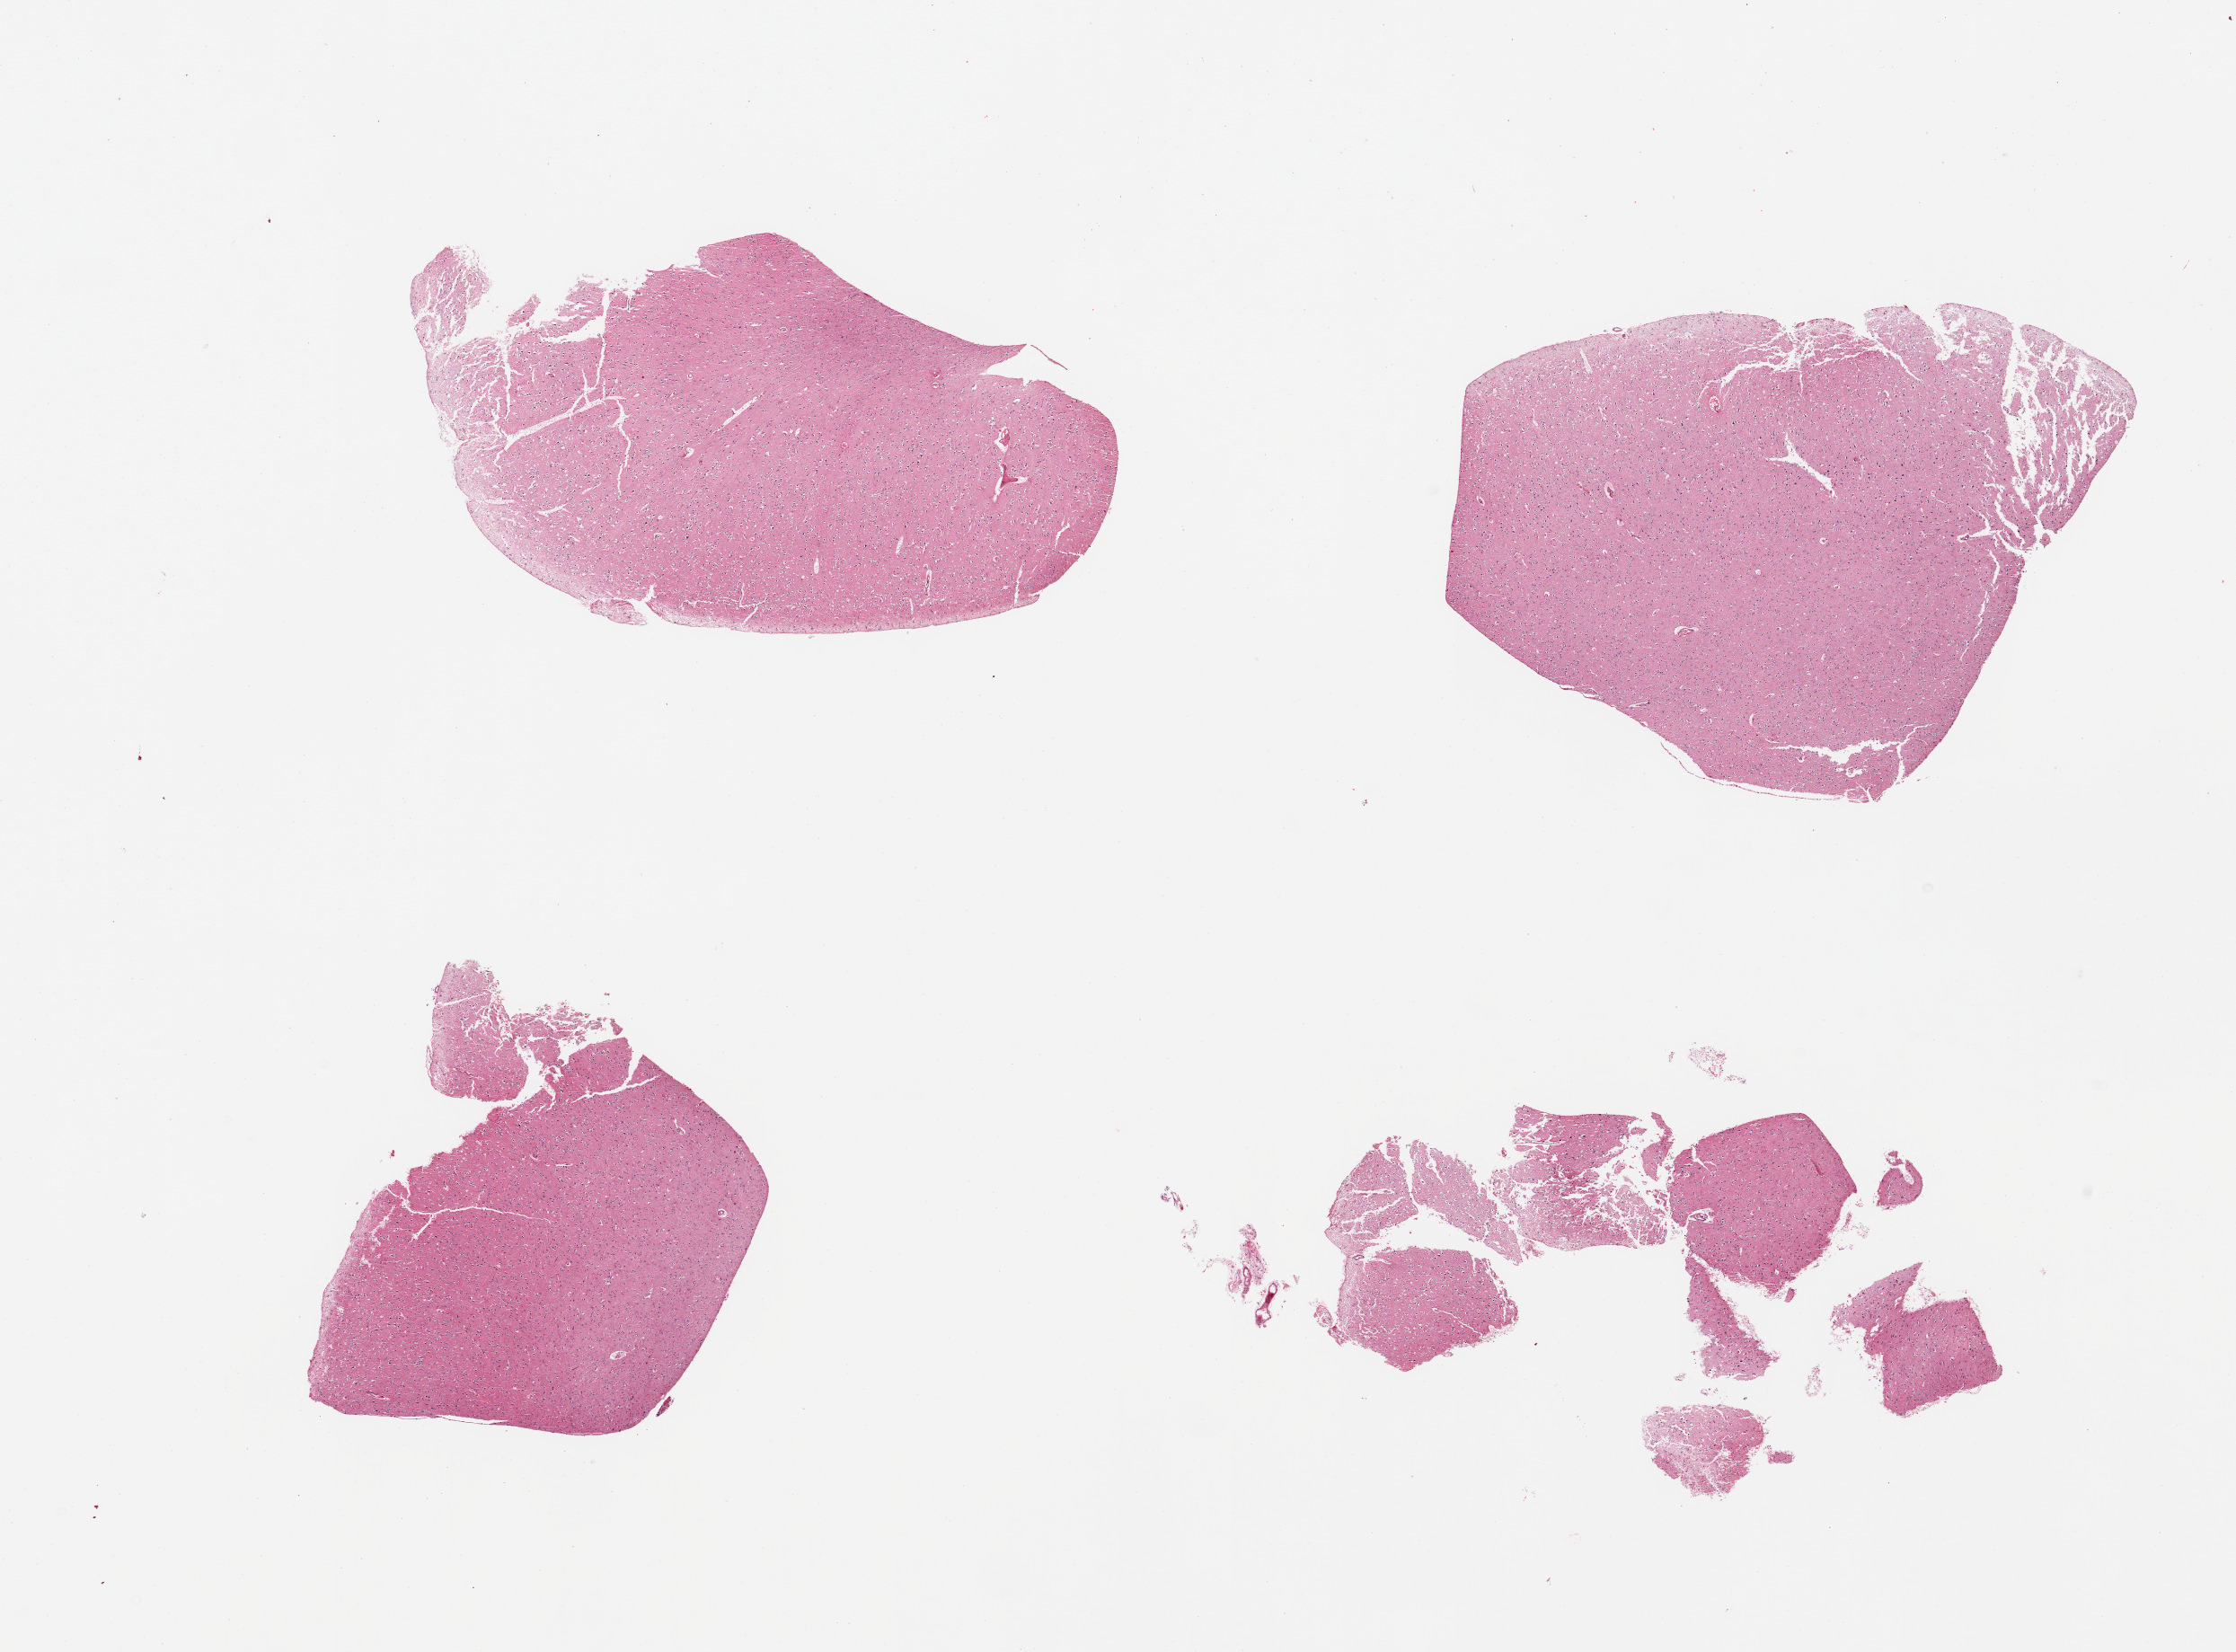
Whole-slide image, hematoxylin and eosin (H&E) stain — whole scanned area (about 19.7 x 14.5 mm, slide scanned at 20x) shown as a low-resolution overview; PAXgene-fixed, paraffin-embedded tissue; target tissue: cerebral cortex; tissue donor sample. Donor sex: male.
Pathologist's review note for this sample: 4 pieces.